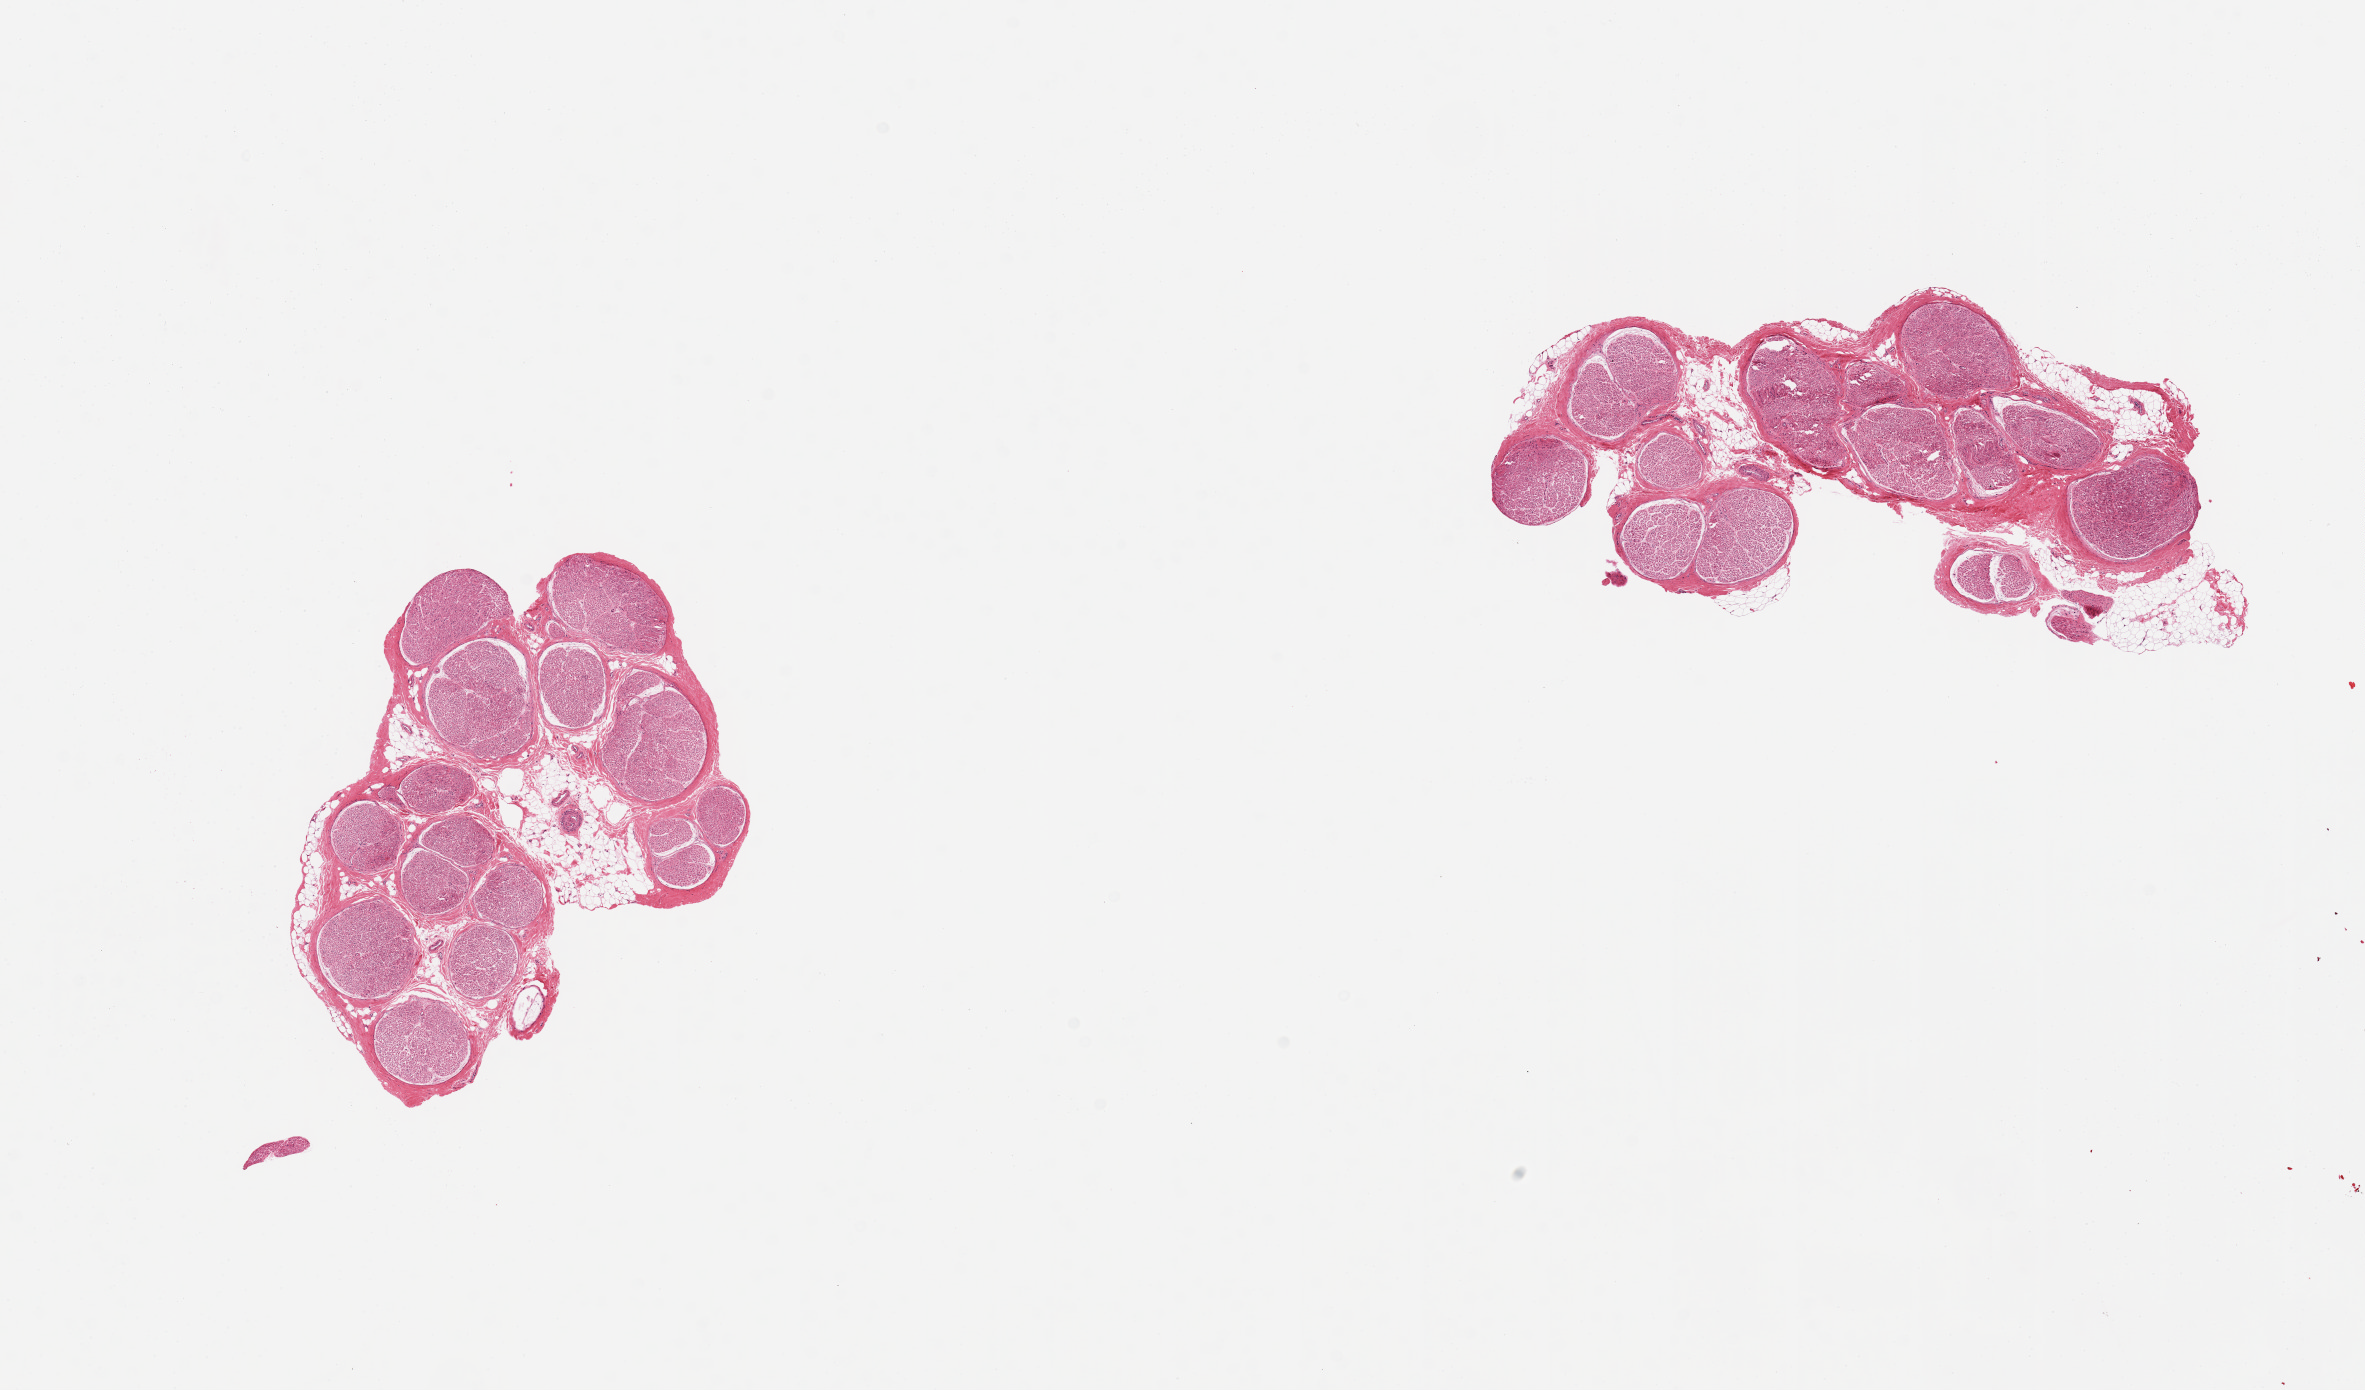
Whole-slide image, haematoxylin and eosin stain — whole scanned area (about 18.7 x 11.0 mm, from a 20x scan) shown as a low-resolution overview. PAXgene-fixed paraffin-embedded (PFPE) section. Section of tibial nerve (target tissue). Tissue donor sample. Female donor.
Review note (as recorded): 2 pieces, clean specimens.